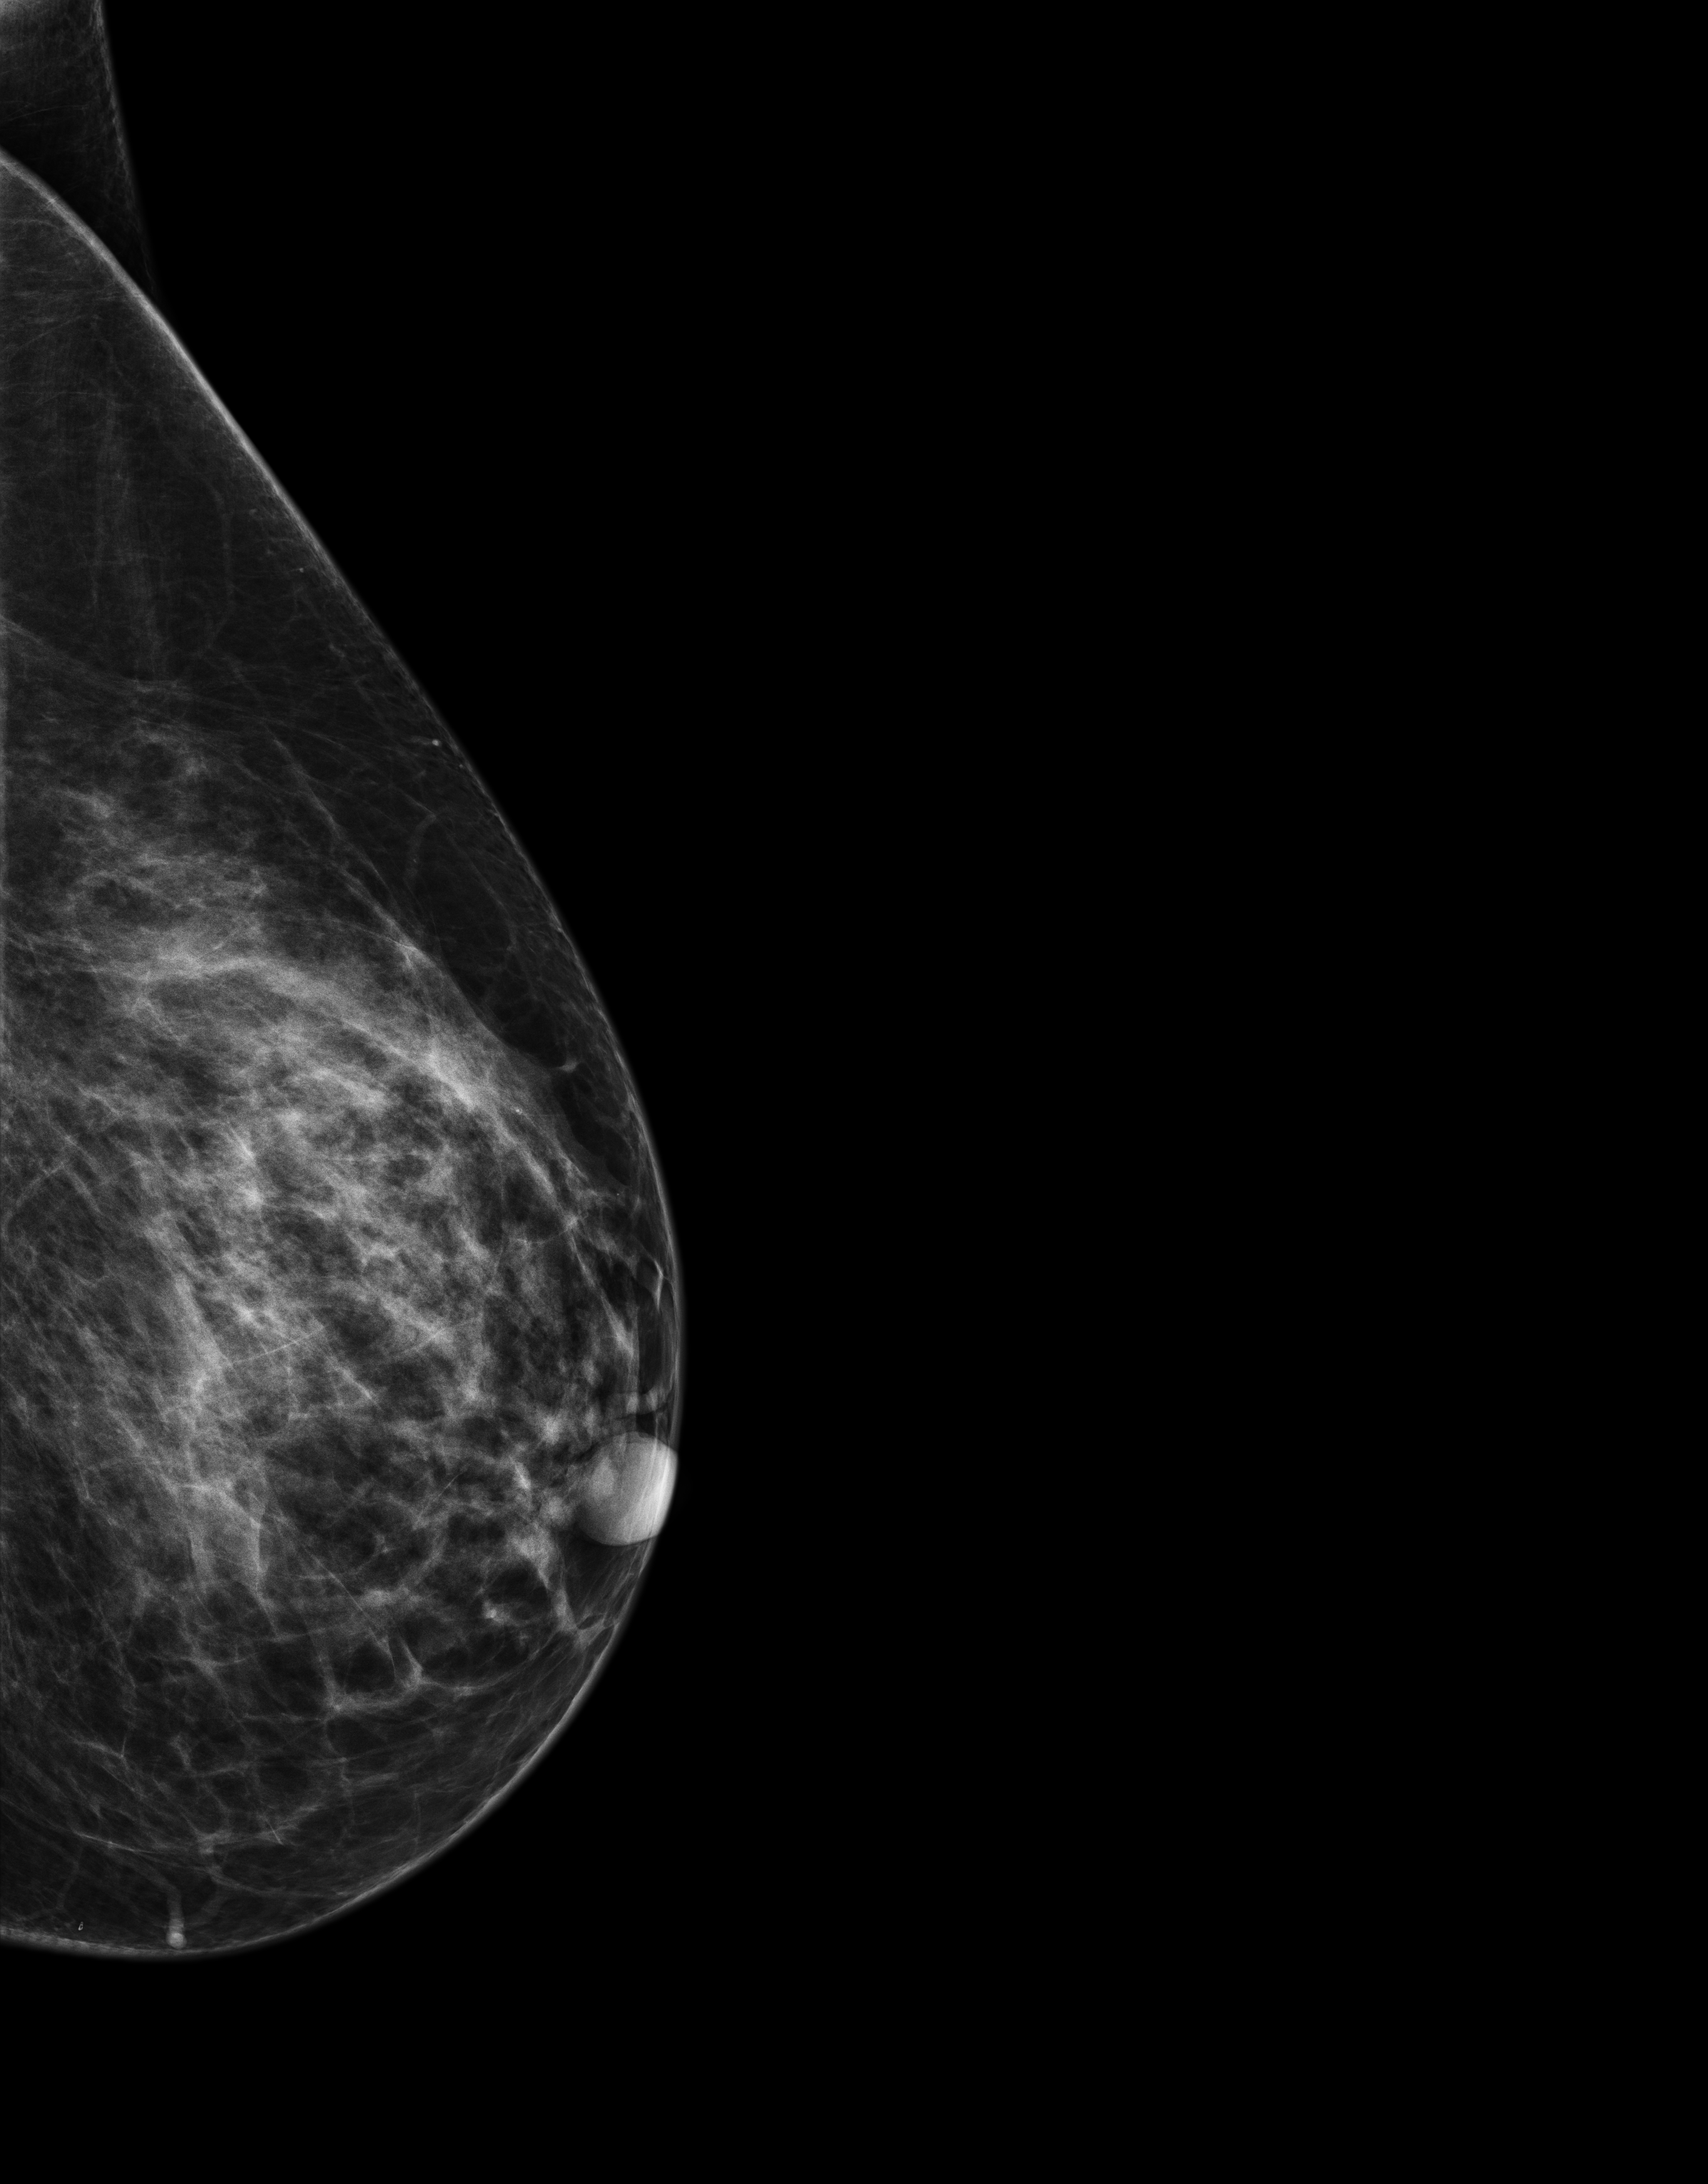
Screening examination. Patient aged 50 years (female).
Image type: full-field digital mammogram. Breast: left. Projection: exaggerated CC view (lateral).